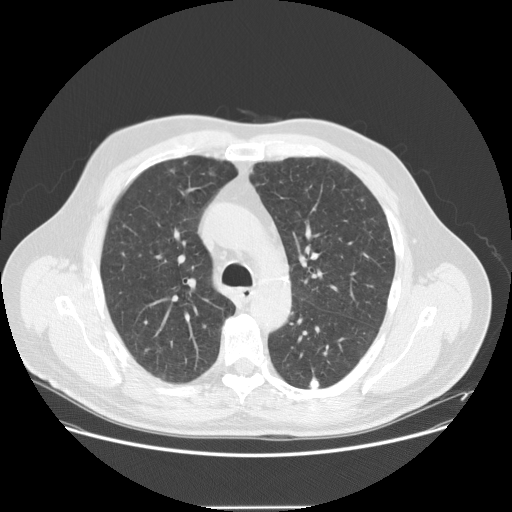
Low-dose screening chest CT, one axial slice. Position 100 of 143 along the scan axis. Lung window (W 1500 / L -600 HU). 2.5 mm slice thickness. 512 × 512 image matrix.
Structures marked on this image (manually delineated by an expert):
- lesion 2 (tumor): bounding box <310,378,320,389> (left, top, right, bottom; pixels)